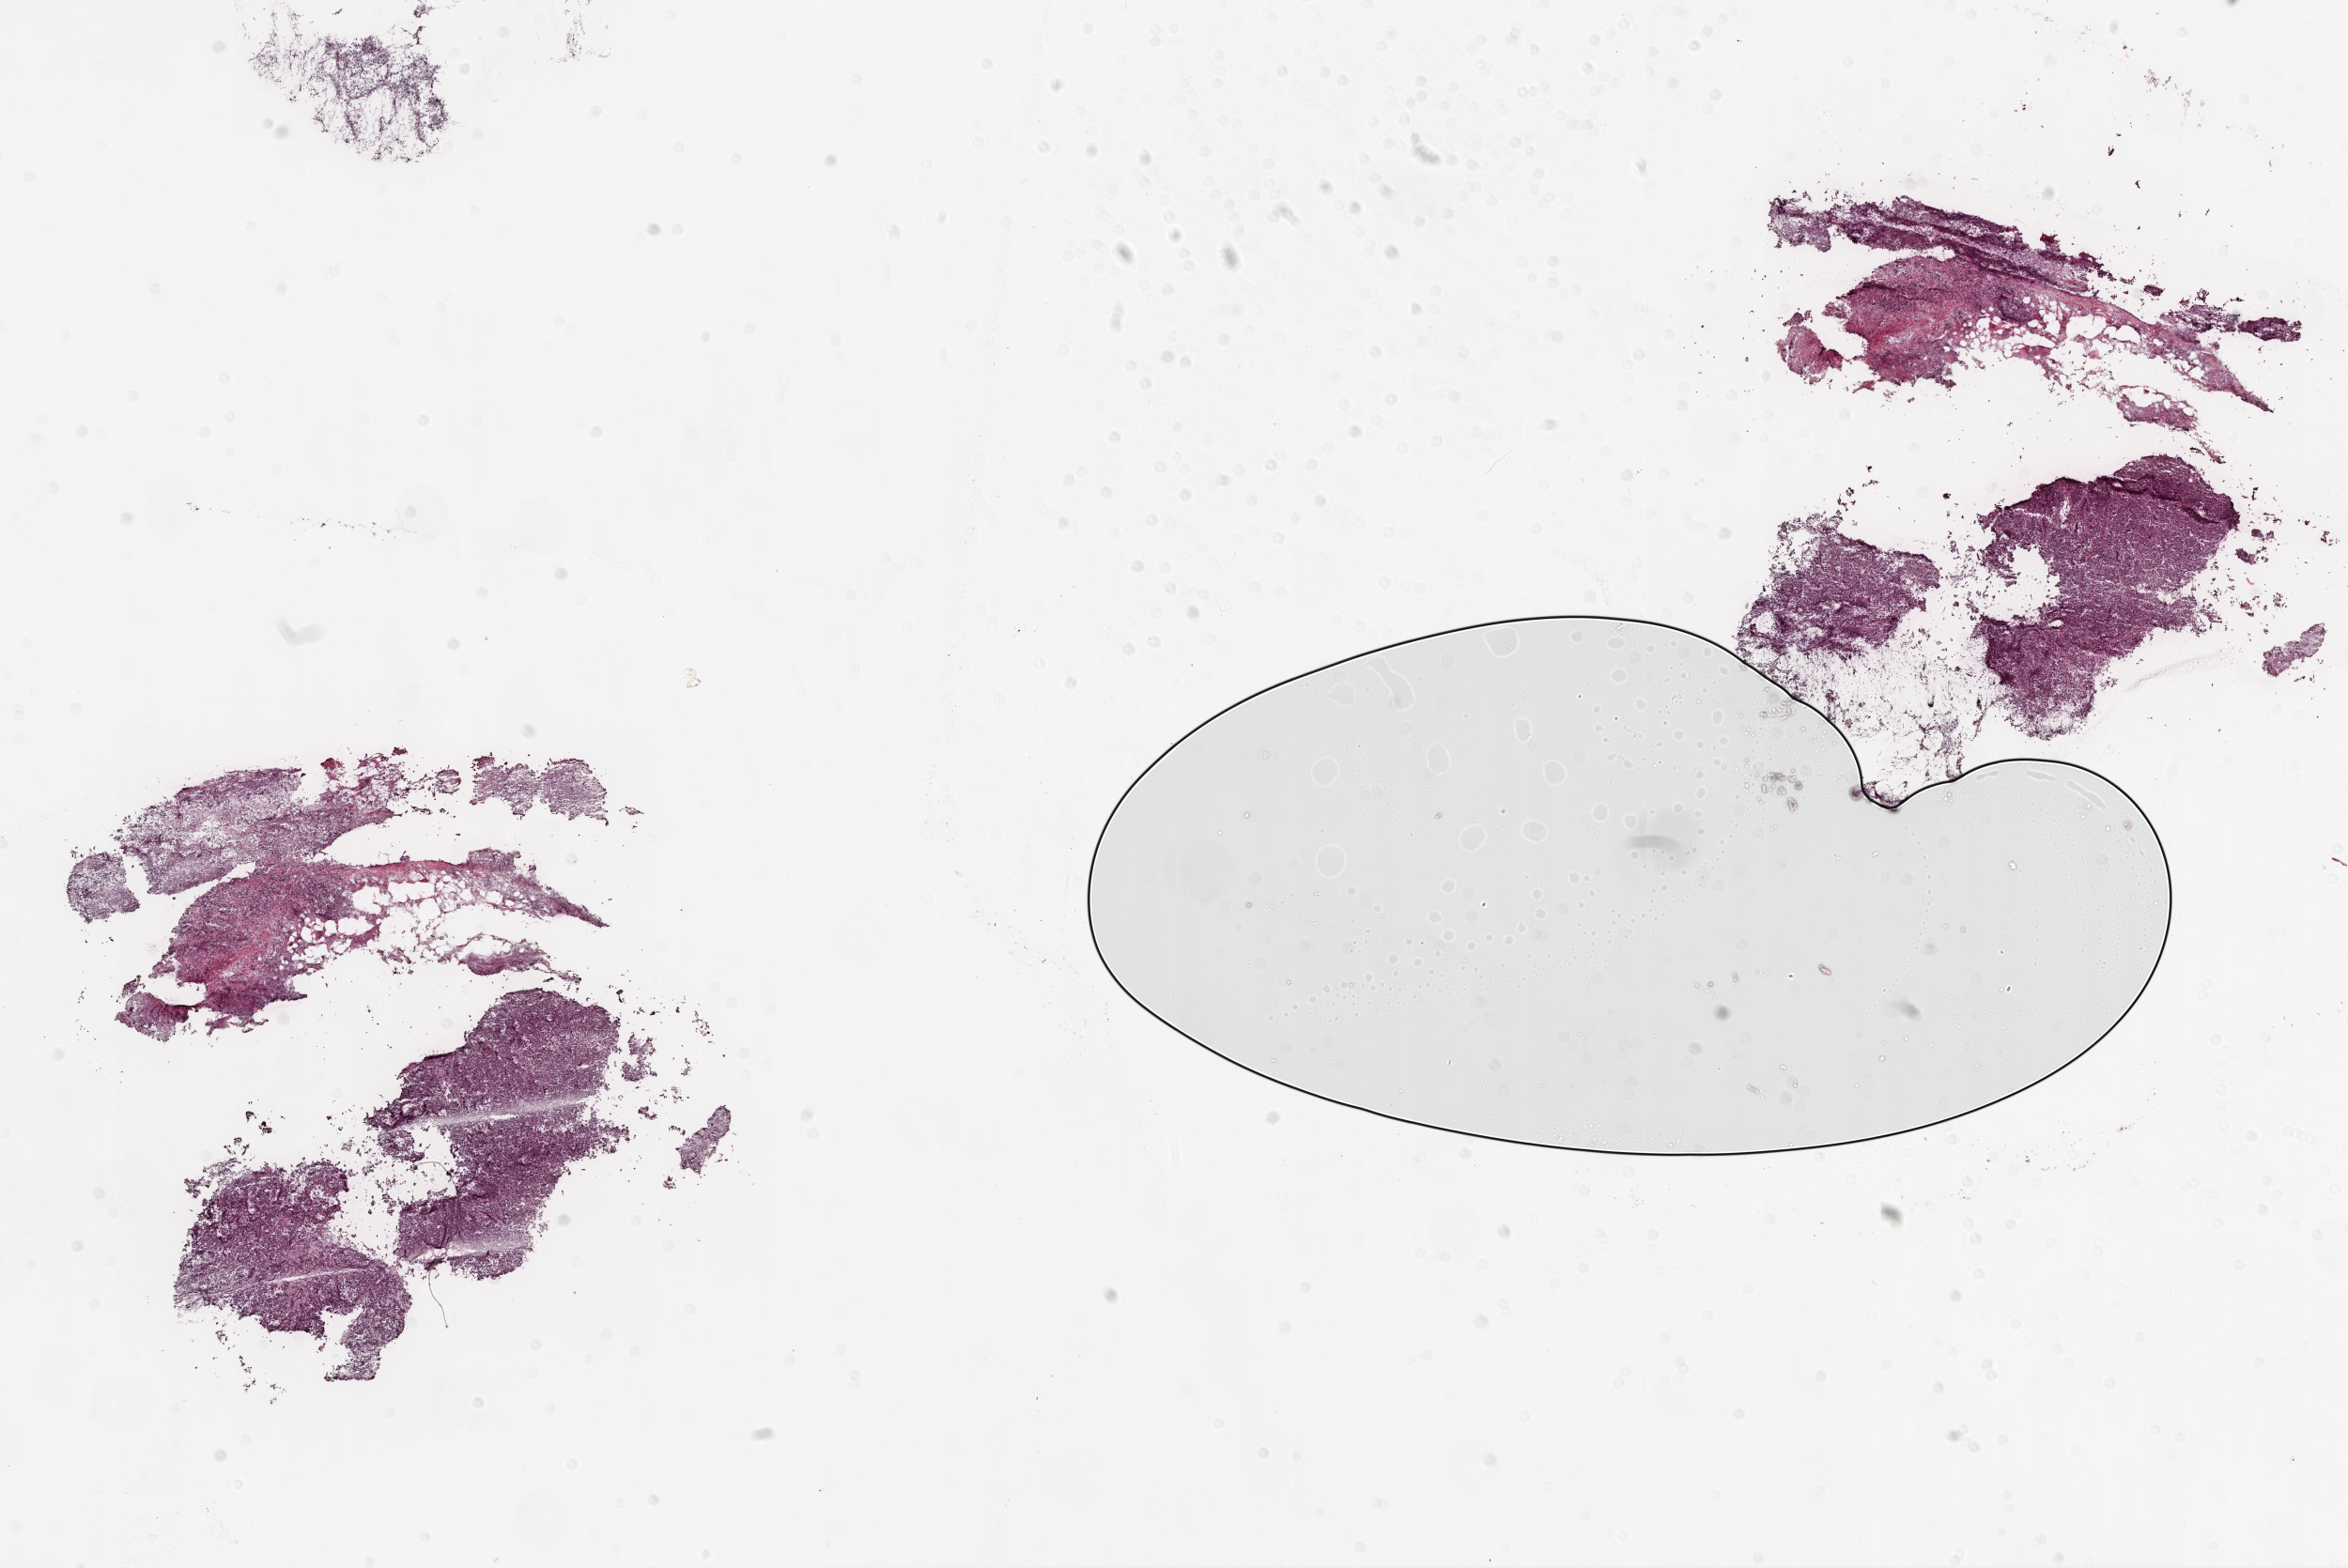
Digitized H&E tissue section (whole slide) — shown as a low-resolution overview of the whole scanned area (about 20.1 x 13.4 mm), frozen section from the top of the tissue portion, primary tumour sample from the ovary. Patient: female, age at initial diagnosis 58 years. Histologic grade: G3 (poorly differentiated). Composition of this section per pathologist review: tumour cells 90%, tumour nuclei 95%, normal cells 0%, stromal cells 10%, necrosis 0%.
FIGO stage: IIIC. Diagnosis: Serous cystadenocarcinoma, NOS.